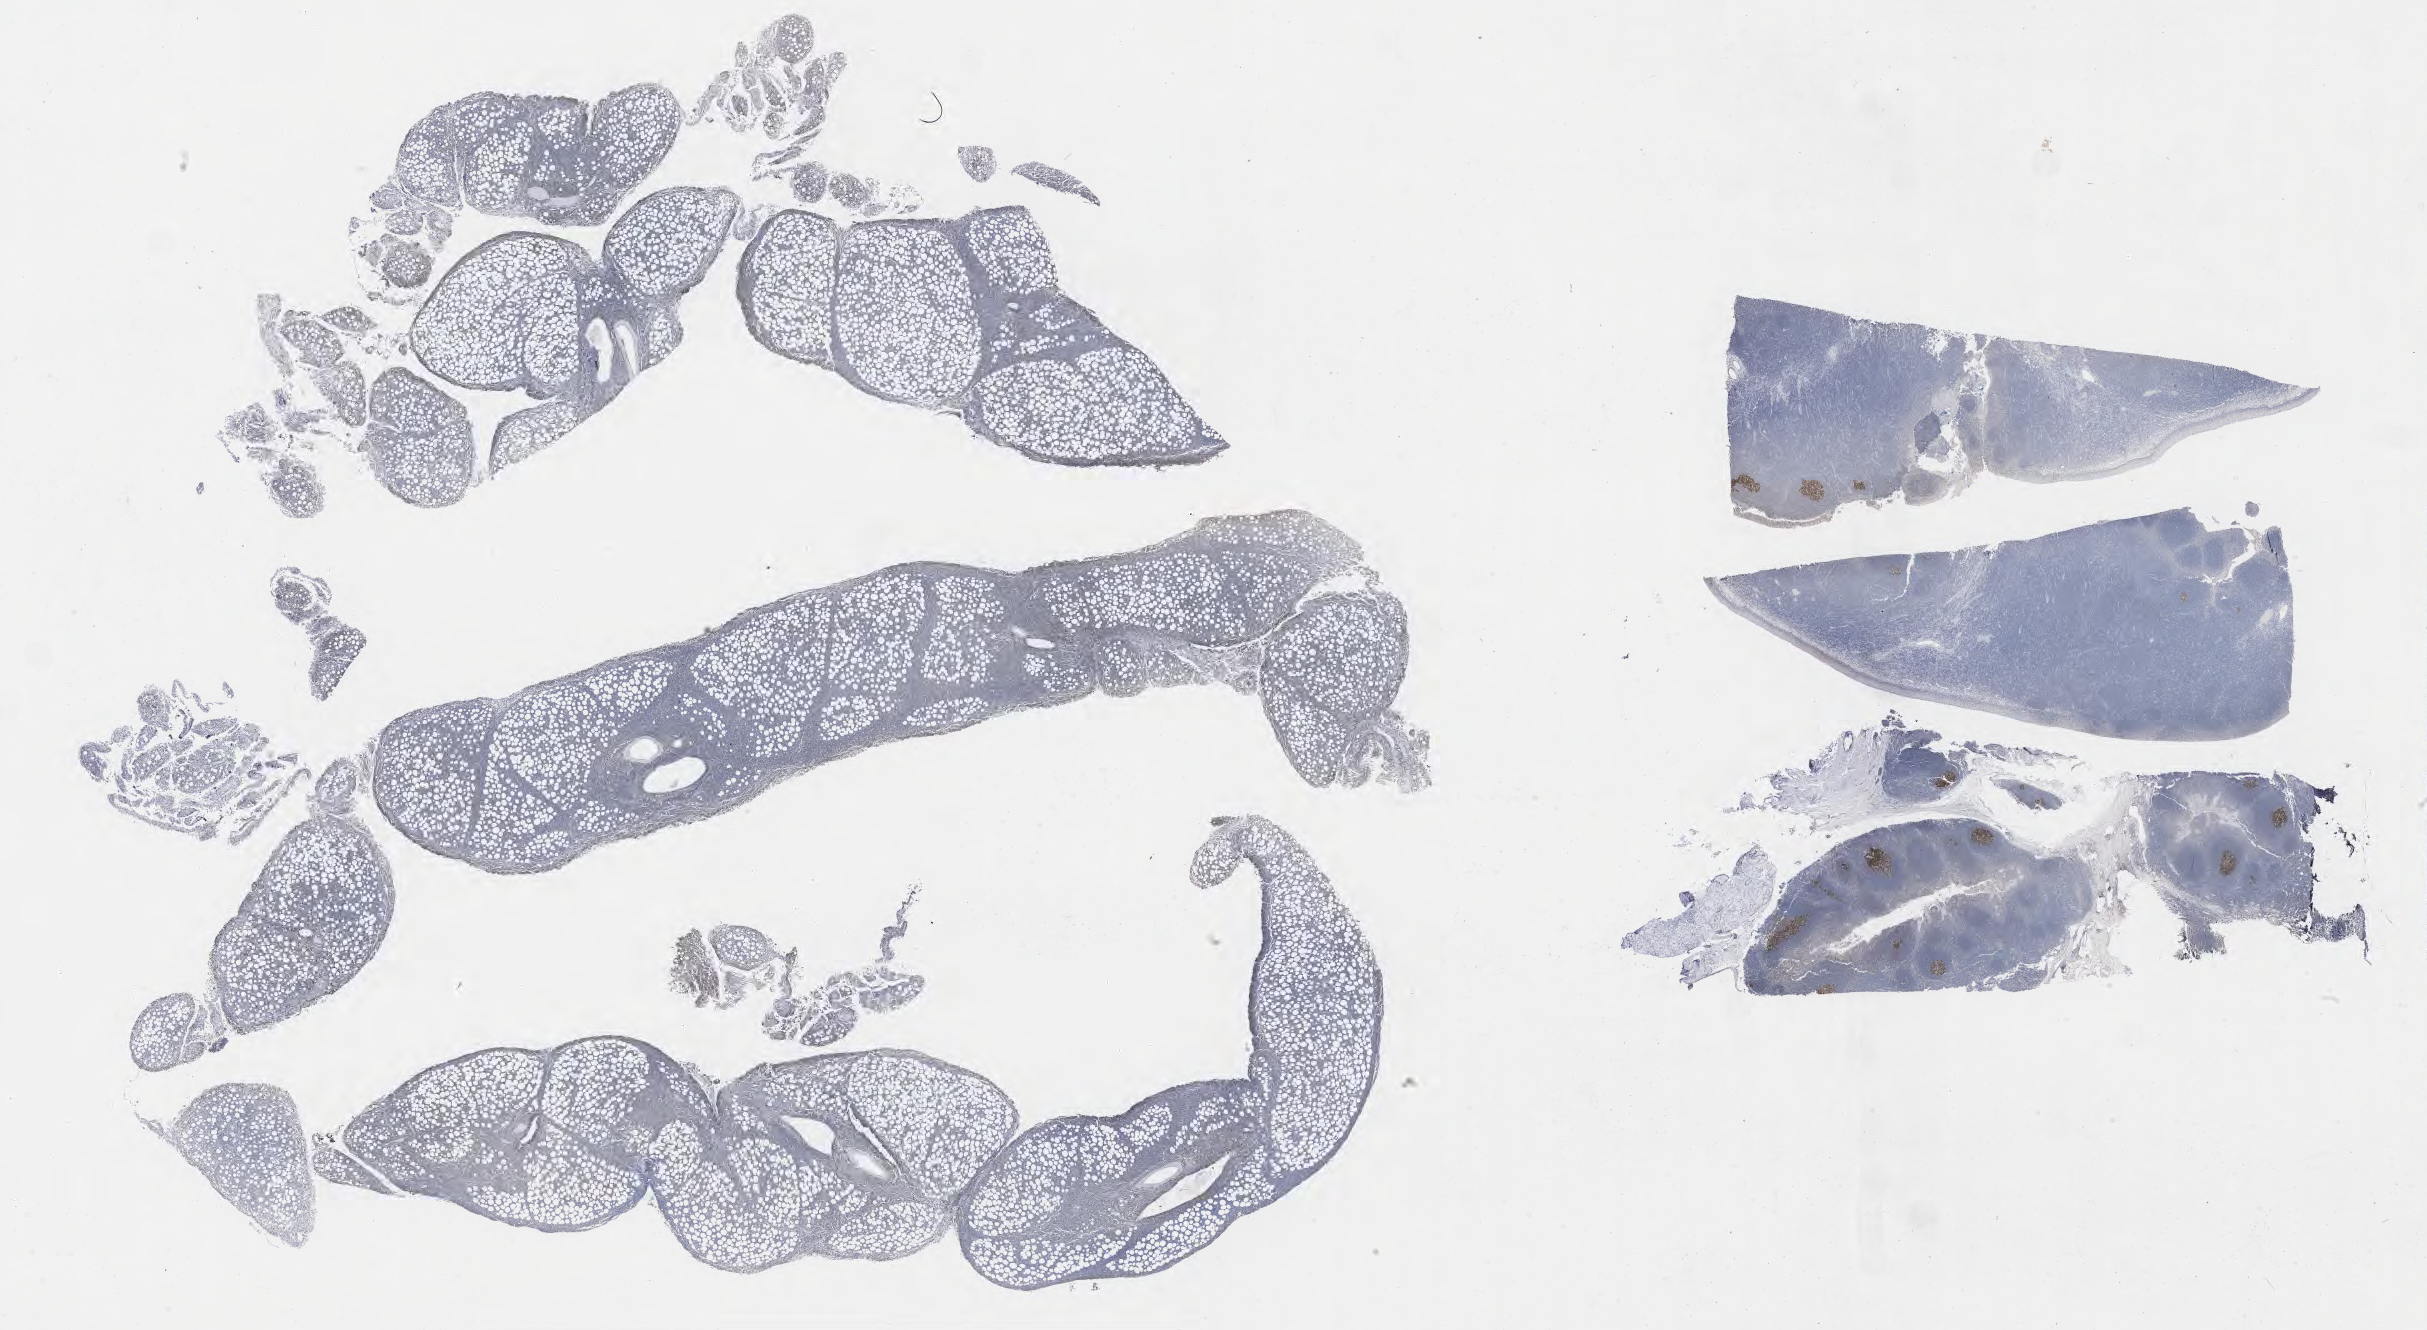
Whole-slide image, immunohistochemical stain for BCL6, whole scanned area (about 39.3 x 21.5 mm) shown as a low-resolution overview. Tumor tissue. Site: abdomen proper. Patient: female, age at initial diagnosis 9 years.
- histologic diagnosis: Burkitt lymphoma, NOS